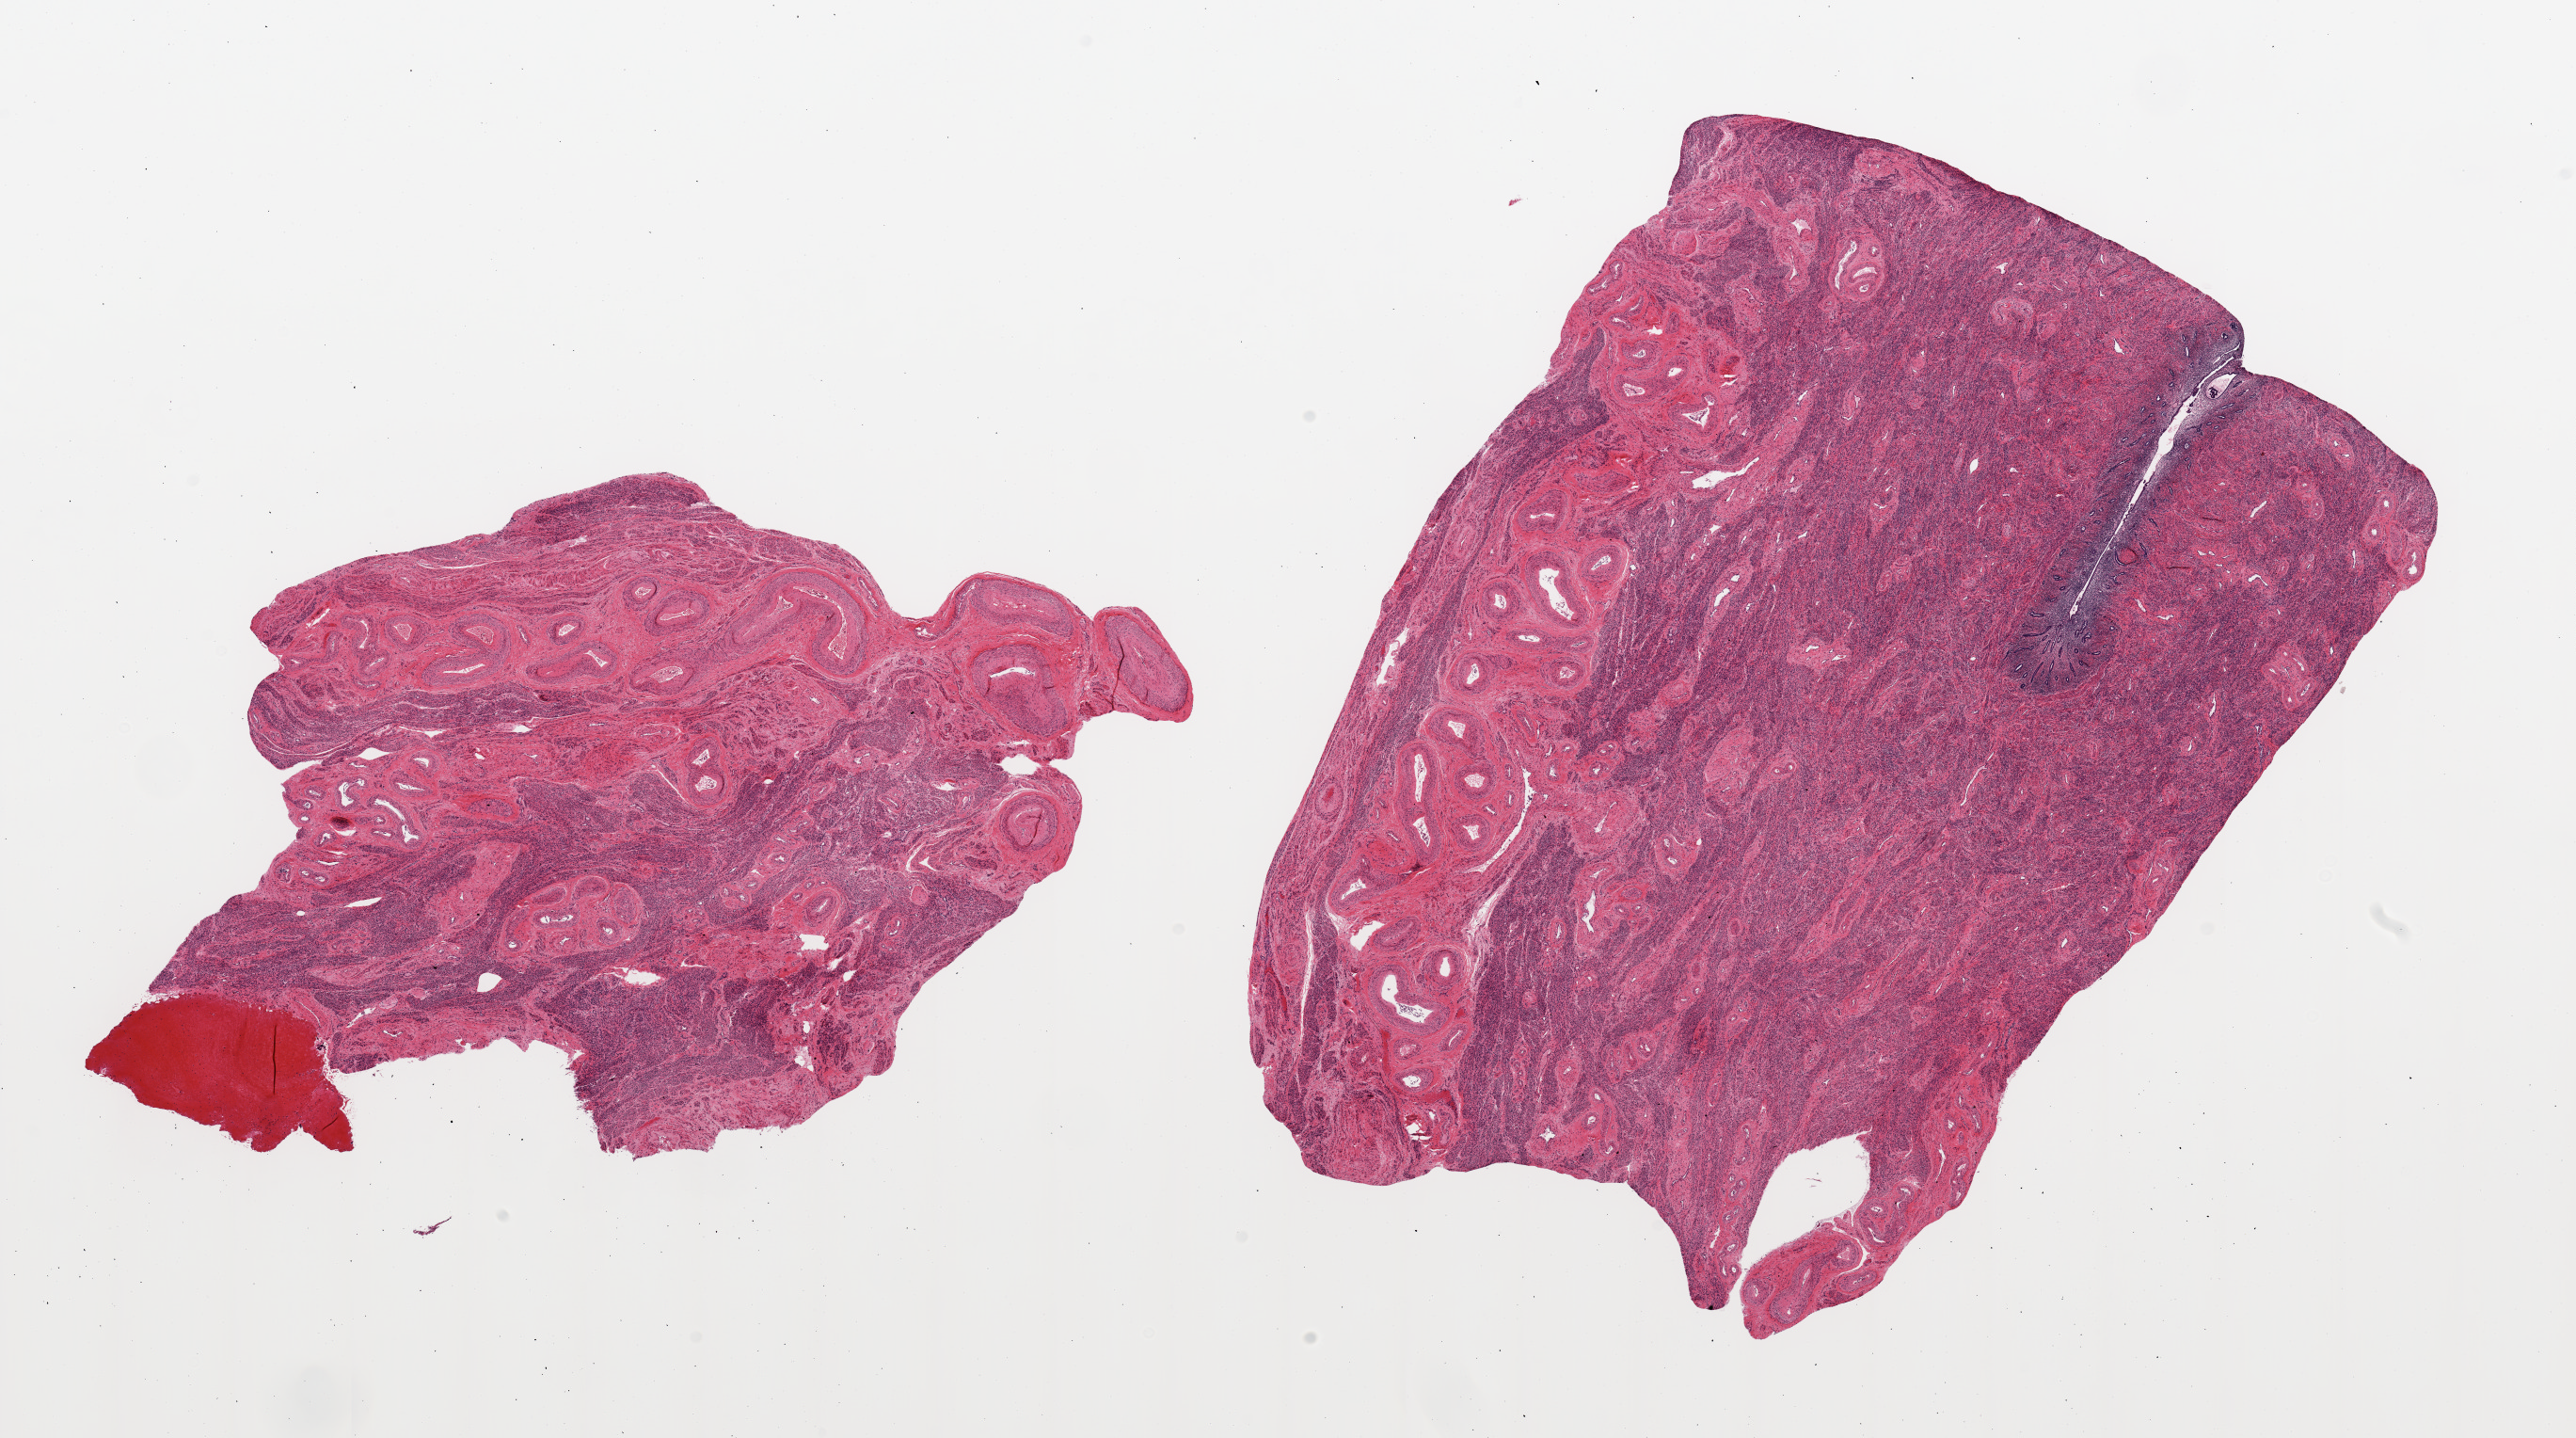
Digitized haematoxylin and eosin-stained section, low-resolution overview of the scanned area, about 21.7 x 12.1 mm; PAXgene-fixed, paraffin-embedded tissue; sampled site (target tissue): uterus; tissue donor sample. Donor sex: female.
Pathologist's review note for this sample: 2 pieces: 1 has thin band of endometrium 3 mm sq remainder is myometrium and blood vessels as is other piece.